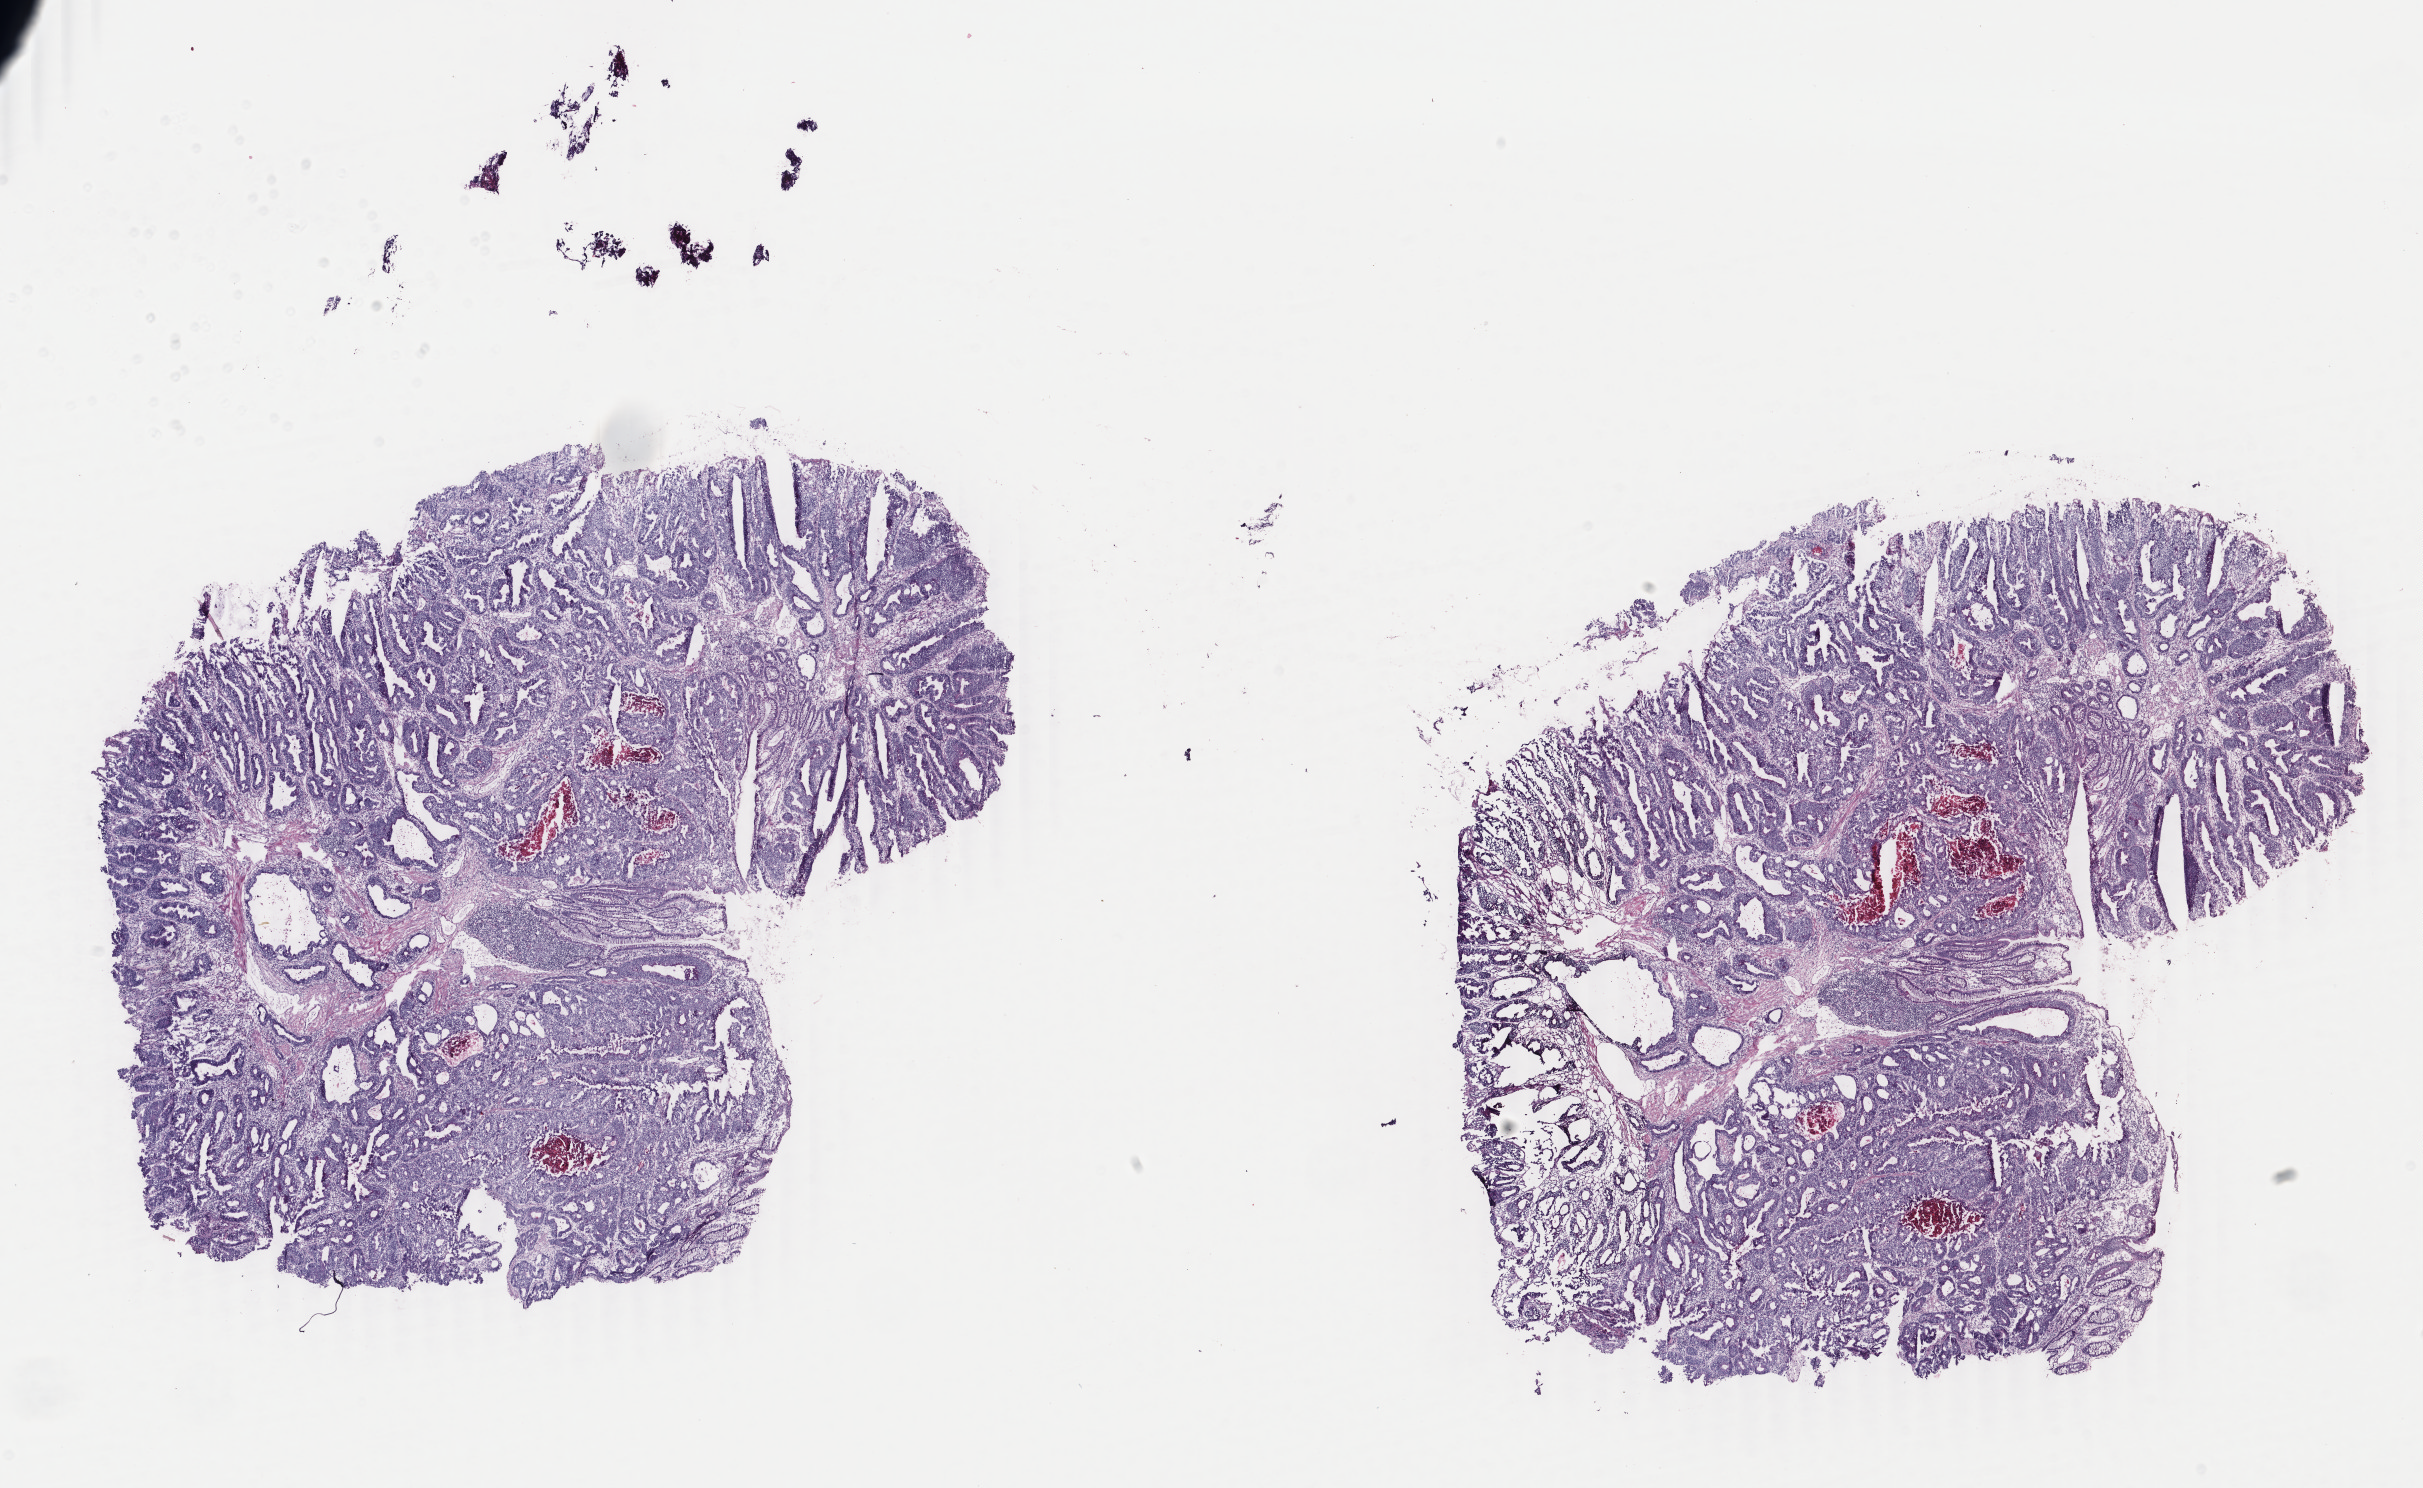
Hematoxylin and eosin (H&E) stained whole-slide image, low-resolution overview of the scanned area, about 19.3 x 11.8 mm; frozen section; sample: primary tumour, colon. Female, age 74 years at initial diagnosis. Composition of this section per pathologist review: tumour cells 80%, tumour nuclei 80%, normal cells 5%, stromal cells 12%, necrosis 3%. Inflammatory infiltration, as recorded: lymphocyte infiltration 3%, monocyte infiltration 0%, neutrophil infiltration 0%.
- AJCC pathologic stage: IV
- TNM: T3 N2 M1
- pathologic diagnosis: Adenocarcinoma, NOS (sigmoid colon)